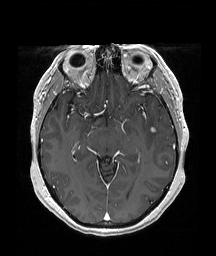
Brain MRI from a brain-tumour surgery series, one axial slice. Slice 112 of 192 in the series (ordered by position). T1-weighted post-contrast. 216 × 256 image matrix, field of view 211 × 250 mm. From the clinical record (not read from this slice): histopathology: Papillary glioneuronal tumor; WHO grade: 1.
Annotated regions visible in this slice (outlined manually by an expert reader):
- tumour: bounding box [x1, y1, x2, y2] px = [150, 127, 155, 132]